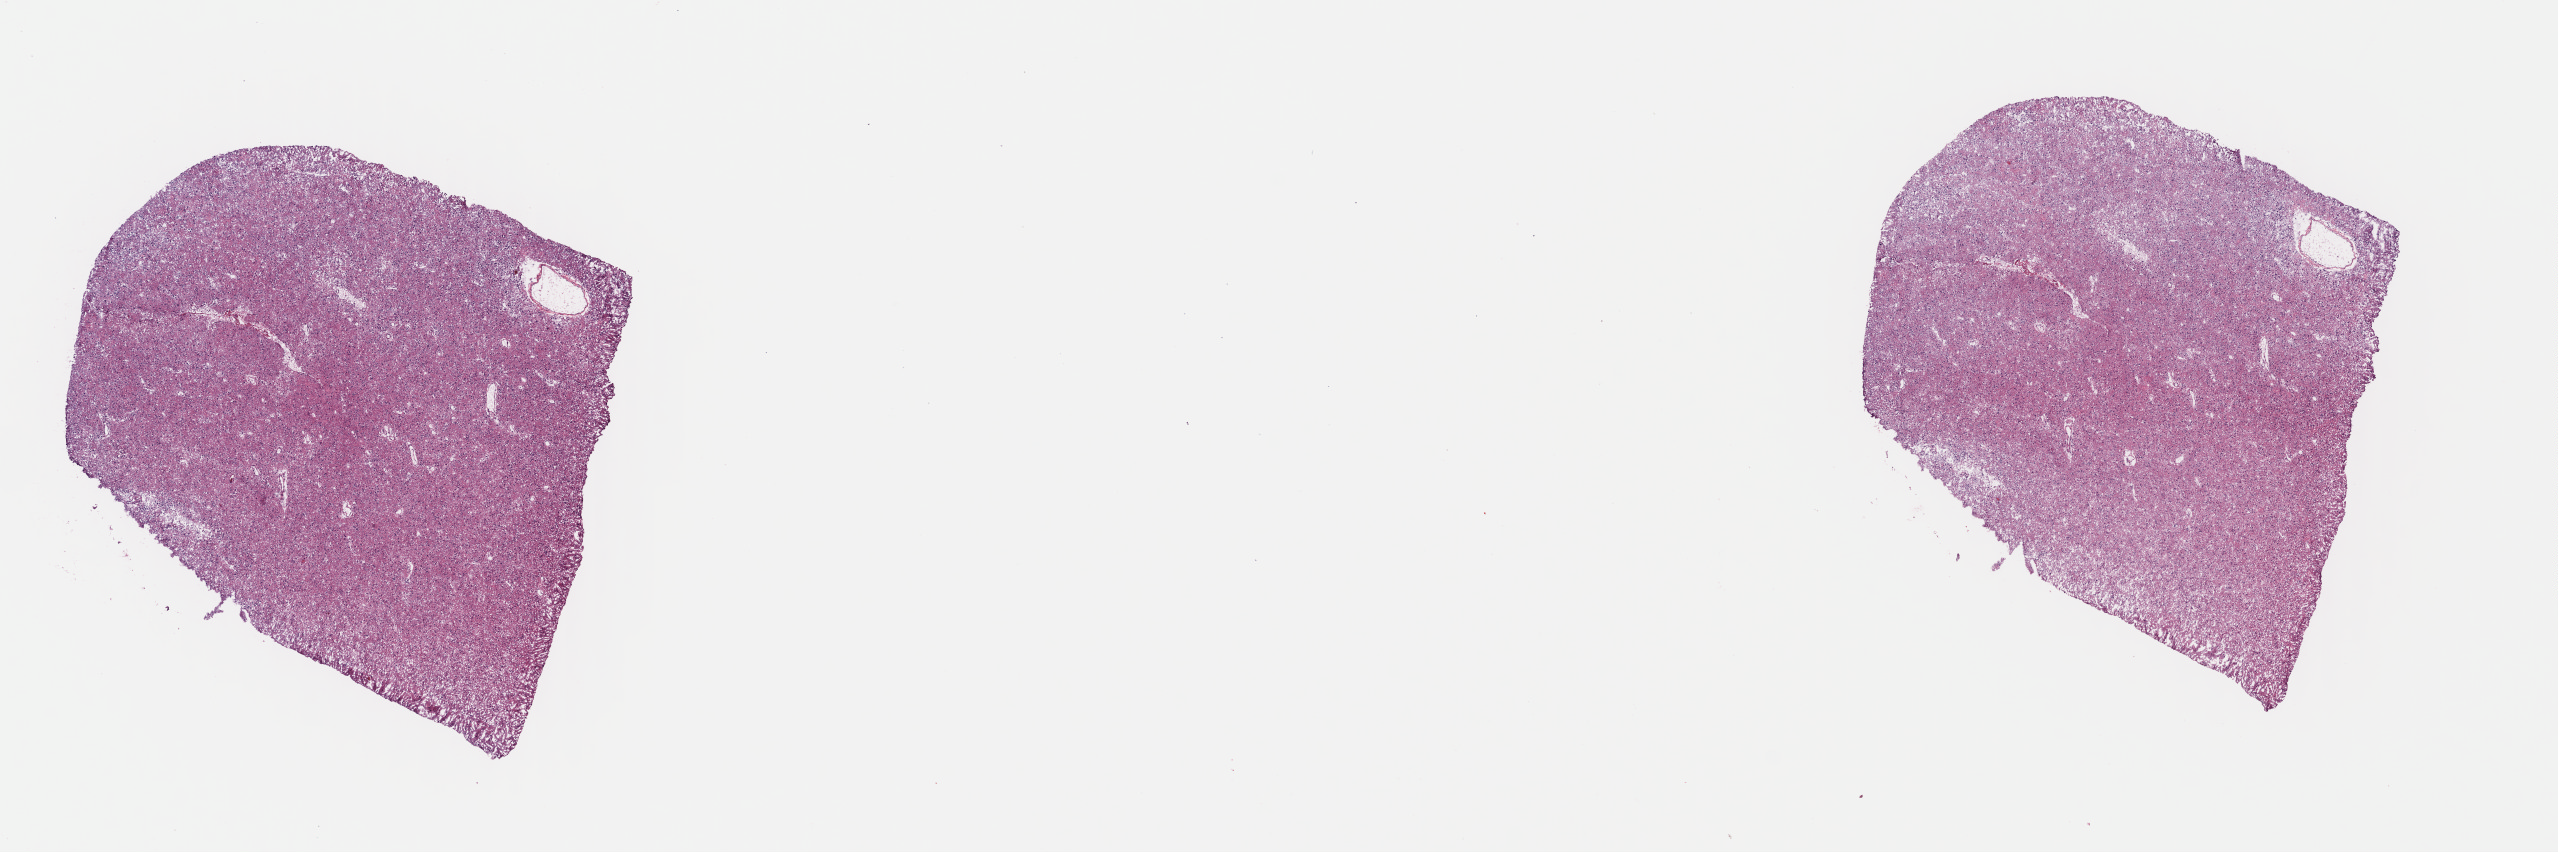
Whole-slide histology image, Hematoxylin and eosin (H&E) stained — whole scanned area (about 20.1 x 6.7 mm, from a 40x scan) shown as a low-resolution overview; frozen section from the top of the tissue portion; sample: primary tumour, brain. Male, age 46 years at initial diagnosis. Histologic grade: G3 (poorly differentiated). Slide review estimates, as recorded: tumour cells 40%, tumour nuclei 80%, normal cells 10%, stromal cells 50%, necrosis 0%. Inflammatory infiltration, as recorded: lymphocyte infiltration 0%, monocyte infiltration 0%, neutrophil infiltration 0%.
- laterality: left
- histologic diagnosis: Oligodendroglioma, anaplastic (cerebrum)